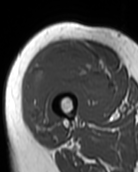
MRI of an extremity soft-tissue mass, one axial slice. Slice 34 of 99 in the series (ordered by position). MR volume resampled by the dataset authors to the PET/CT grid (not the native acquisition matrix). 3.27 mm slice thickness. 138 × 172 image matrix, field of view 135 × 168 mm. Female patient. From the clinical record (not read from this slice): histological type: pleiomorphic undifferentiated sarcoma; grade: high; site of the primary tumour: right quadricep.
Outlined on this slice (expert contour drawn on MRI and transferred to this co-registered scan by the dataset authors):
- gross tumour volume including surrounding oedema: bounding box (x1, y1, x2, y2) in pixels: (25, 45, 109, 131)
- gross tumour volume (mass): (25, 45, 109, 131)